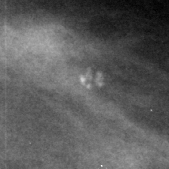
Cropped region of a digitized screen-film mammogram centred on a radiologist-marked abnormality; left breast; CC view.
- Marked abnormality: calcifications, morphology punctate / pleomorphic, distribution clustered; BI-RADS assessment category 4; subtlety rating 3 on a 1 (subtle) to 5 (obvious) scale; pathology result (as recorded, not read from the image): benign.